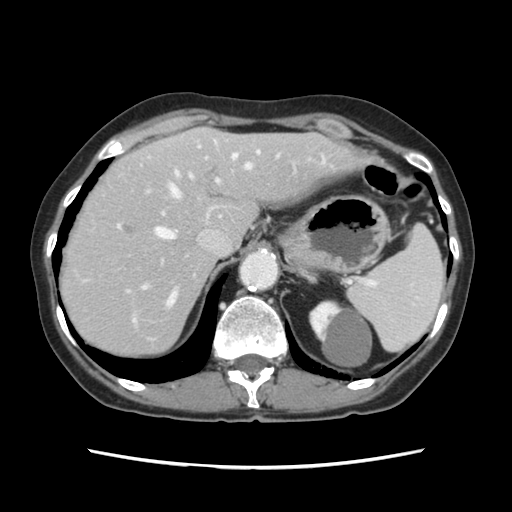
Contrast-enhanced abdominal CT, one axial slice. Slice 90 of 120 in the series (ordered by position). Soft-tissue window (W 400 / L 40 HU). 512 × 512 image matrix. Female patient, age 70 years. Case-level facts recorded for this patient, not image findings: diagnosis: colorectal cancer liver metastases, imaged before liver resection; multiple liver metastases: no; largest metastasis: 2.5 cm.
Structures marked on this image (expert manual segmentation):
- hepatic veins: bounding box (x1, y1, x2, y2) in pixels: (156, 154, 251, 309)
- liver: (62, 129, 355, 354)
- planned liver remnant (the part of the liver to remain after resection): (123, 129, 354, 287)
- portal vein (with intrahepatic branches): (117, 146, 259, 323)
- liver metastasis: (123, 225, 133, 234)